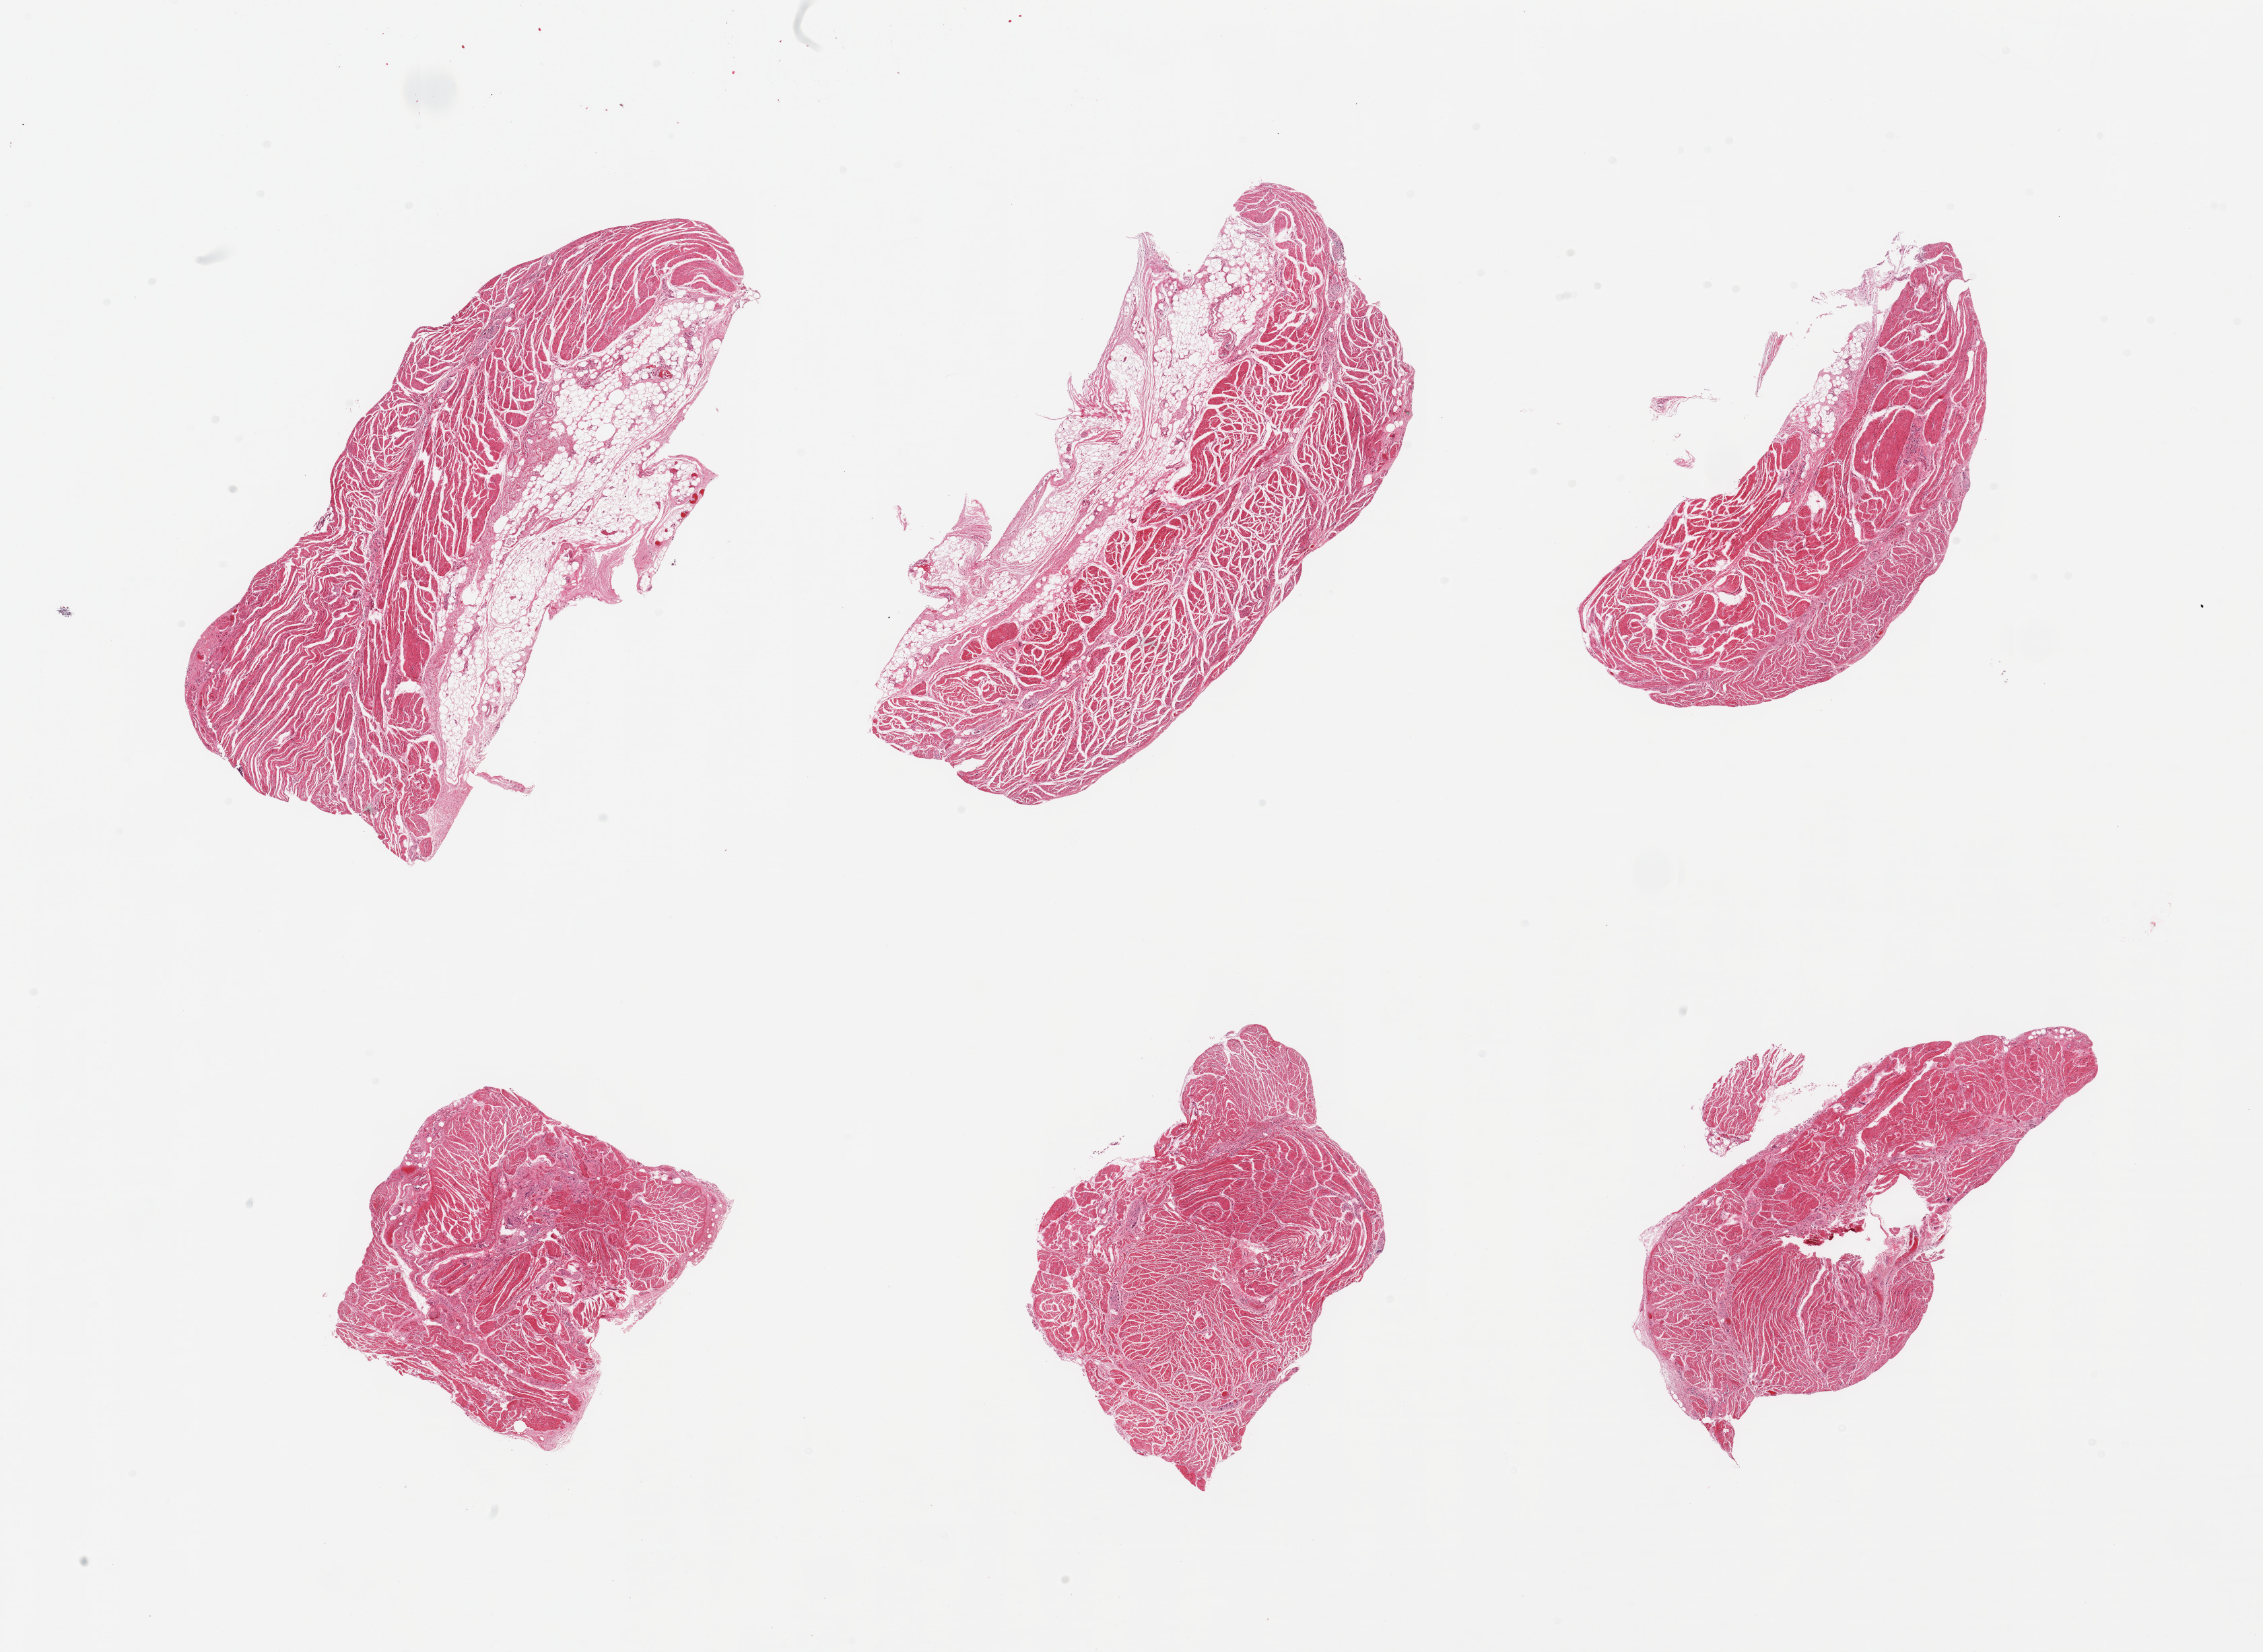
Whole-slide image, haematoxylin and eosin stain, low-resolution overview of the scanned area, about 26.6 x 19.4 mm (from a 20x scan), PAXgene-fixed, paraffin-embedded tissue, sampled site (target tissue): gastroesophageal junction, donor tissue sample.
Pathologist's review note for this sample: 6 pieces; target muscularis and two pieces with attached fat/vessels up to 2mm.